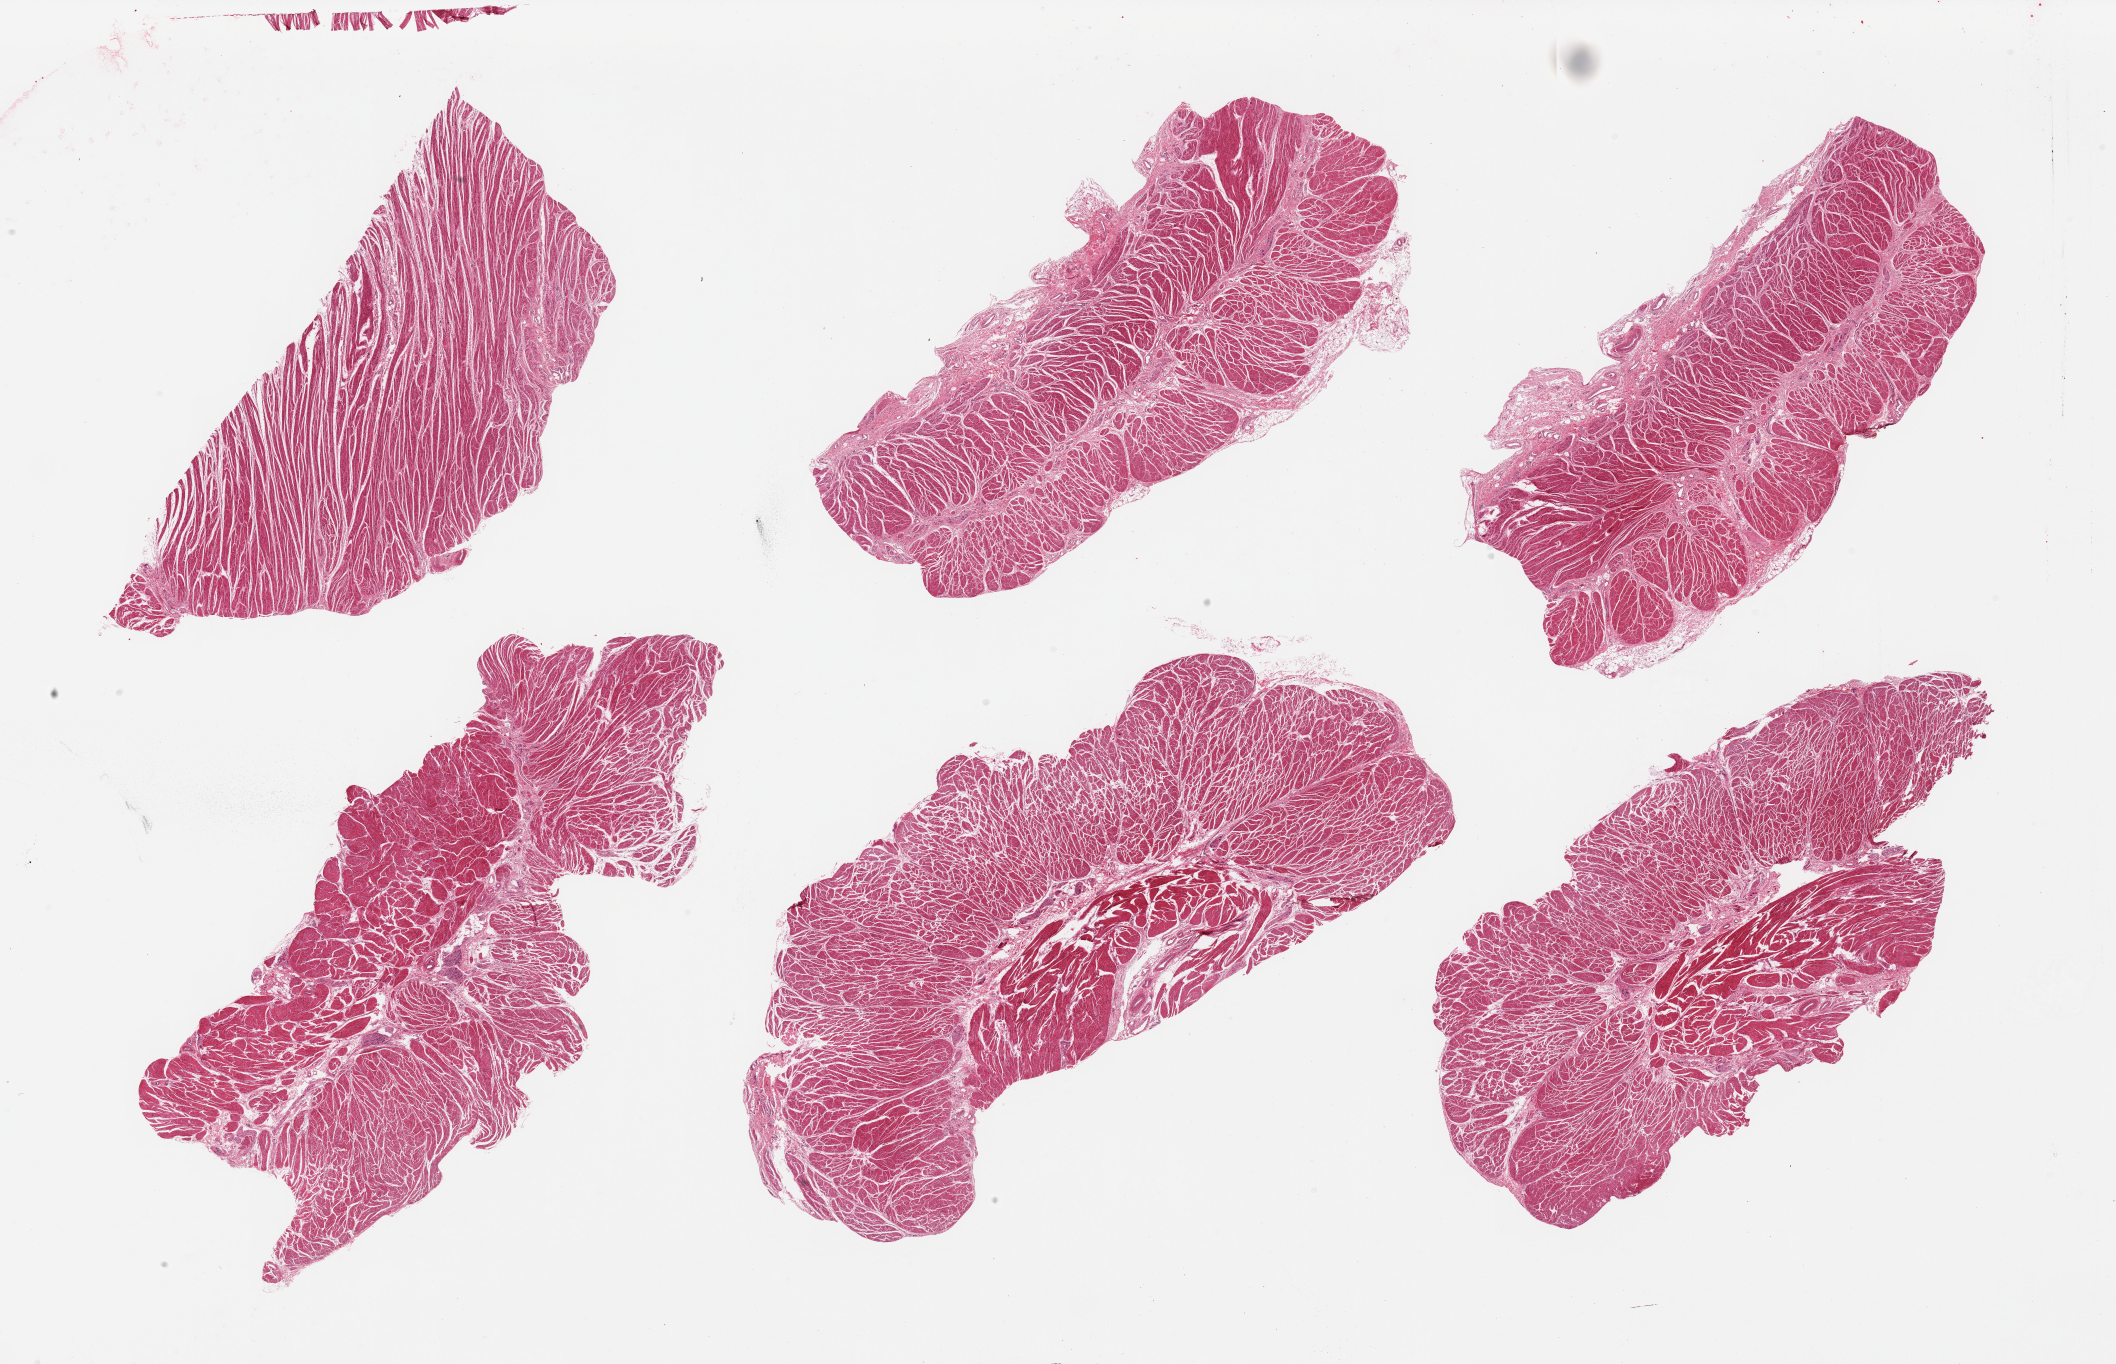
Digitized hematoxylin and eosin (H&E)-stained section, whole scanned area (about 33.5 x 21.6 mm, from a 20x scan) shown as a low-resolution overview; PAXgene-fixed, paraffin-embedded tissue; sampled site (target tissue): gastroesophageal junction; tissue donor sample.
- reviewer comment on this tissue sample: 6 pieces; well trimmed muscle